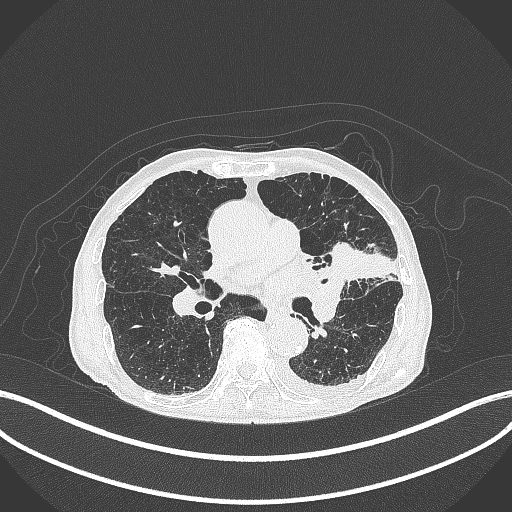
Chest CT, one axial slice. Position 203 of 385 along the scan axis. Reconstruction kernel B70f. 120 kVp. Lung window (W 1500 / L -600 HU). 512 × 512 image matrix, field of view 400 × 400 mm. Patient: male, 90 years or older. Case-level facts recorded for this patient, not image findings: clinical TNM (as recorded): T2b N1 M0.
Outlined on this slice (bounding box drawn by a radiologist):
- lung tumour (recorded histology: squamous cell carcinoma): bounding box <321,236,378,285> (left, top, right, bottom; pixels)